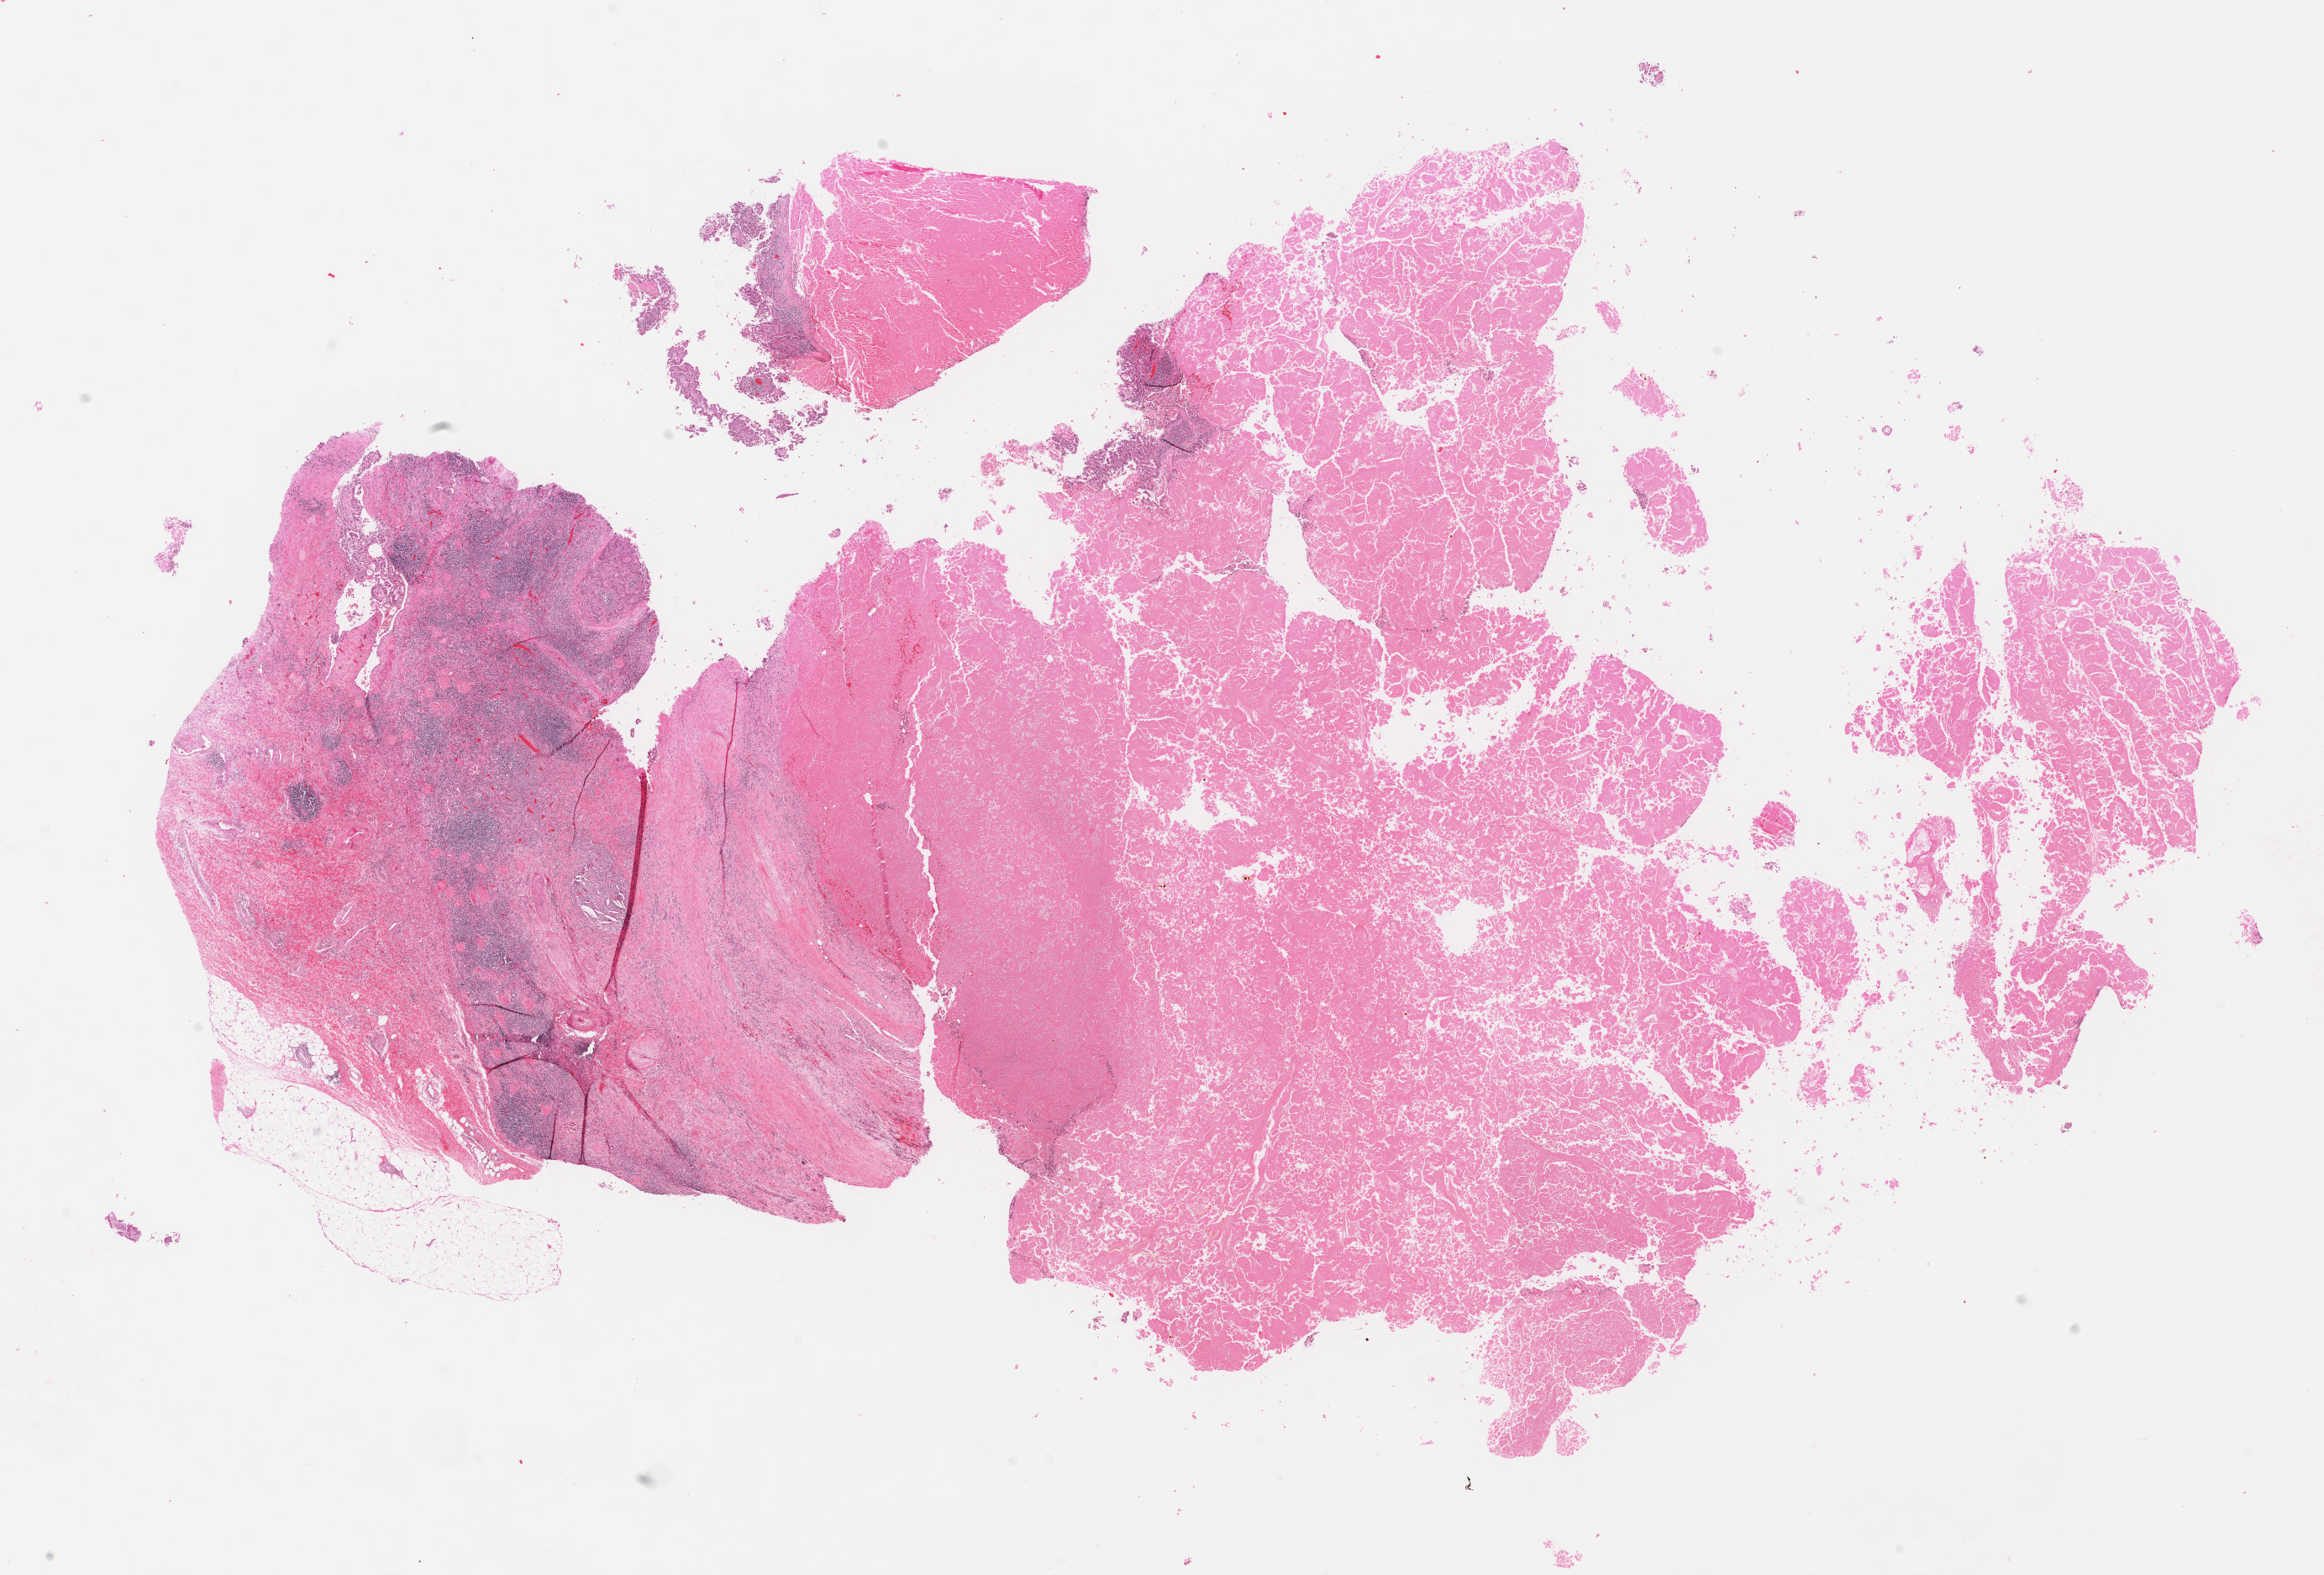
H&E whole-slide image, whole scanned area (about 21.7 x 14.7 mm, slide scanned at 40x) shown as a low-resolution overview, formalin-fixed paraffin-embedded (FFPE) diagnostic section, sample: primary tumour, kidney. Female, age 54 years at initial diagnosis.
TNM: T3a NX MX. Laterality: left. AJCC pathologic stage: III (3rd edition). Diagnosis: Papillary adenocarcinoma, NOS.